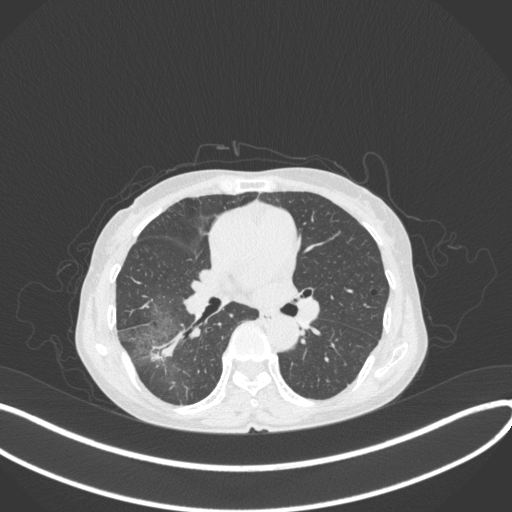
Chest CT, one axial slice. Slice 215 of 379 in the series (ordered by position). 120 kVp. Lung window (W 1500 / L -600 HU). 1 mm slice thickness. 512 × 512 image matrix, field of view 400 × 400 mm. Female patient, age 69 years. Case-level facts recorded for this patient, not image findings: clinical TNM (as recorded): T1b N0 M0; histopathological grade: G2-3.
Annotated regions visible in this slice (rectangle marked by the reading radiologist):
- lung tumour (recorded histology: adenocarcinoma): box from (x=148, y=328) to (x=187, y=365) px